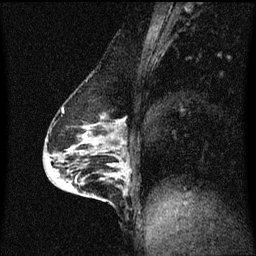
Breast MRI (dynamic contrast-enhanced), one sagittal slice. Position 29 of 60 along the scan axis. Dynamic contrast-enhanced series, image 2 of 3 at this slice position (ordered by acquisition). 1.5 T. TE 4.2 ms, TR 8.4 ms. 2 mm slice thickness. 256 × 256 image matrix. Female patient, age 64 years.
Structures marked on this image (semi-automatically segmented with operator editing):
- analysis volume of interest (the breast-tissue region the enhancement analysis was run in; not a lesion): bounding box [x1, y1, x2, y2] px = [90, 164, 129, 203]
- tumour enhancement mask (voxels above the 70 % enhancement threshold inside the analysis volume of interest): [118, 166, 129, 193]